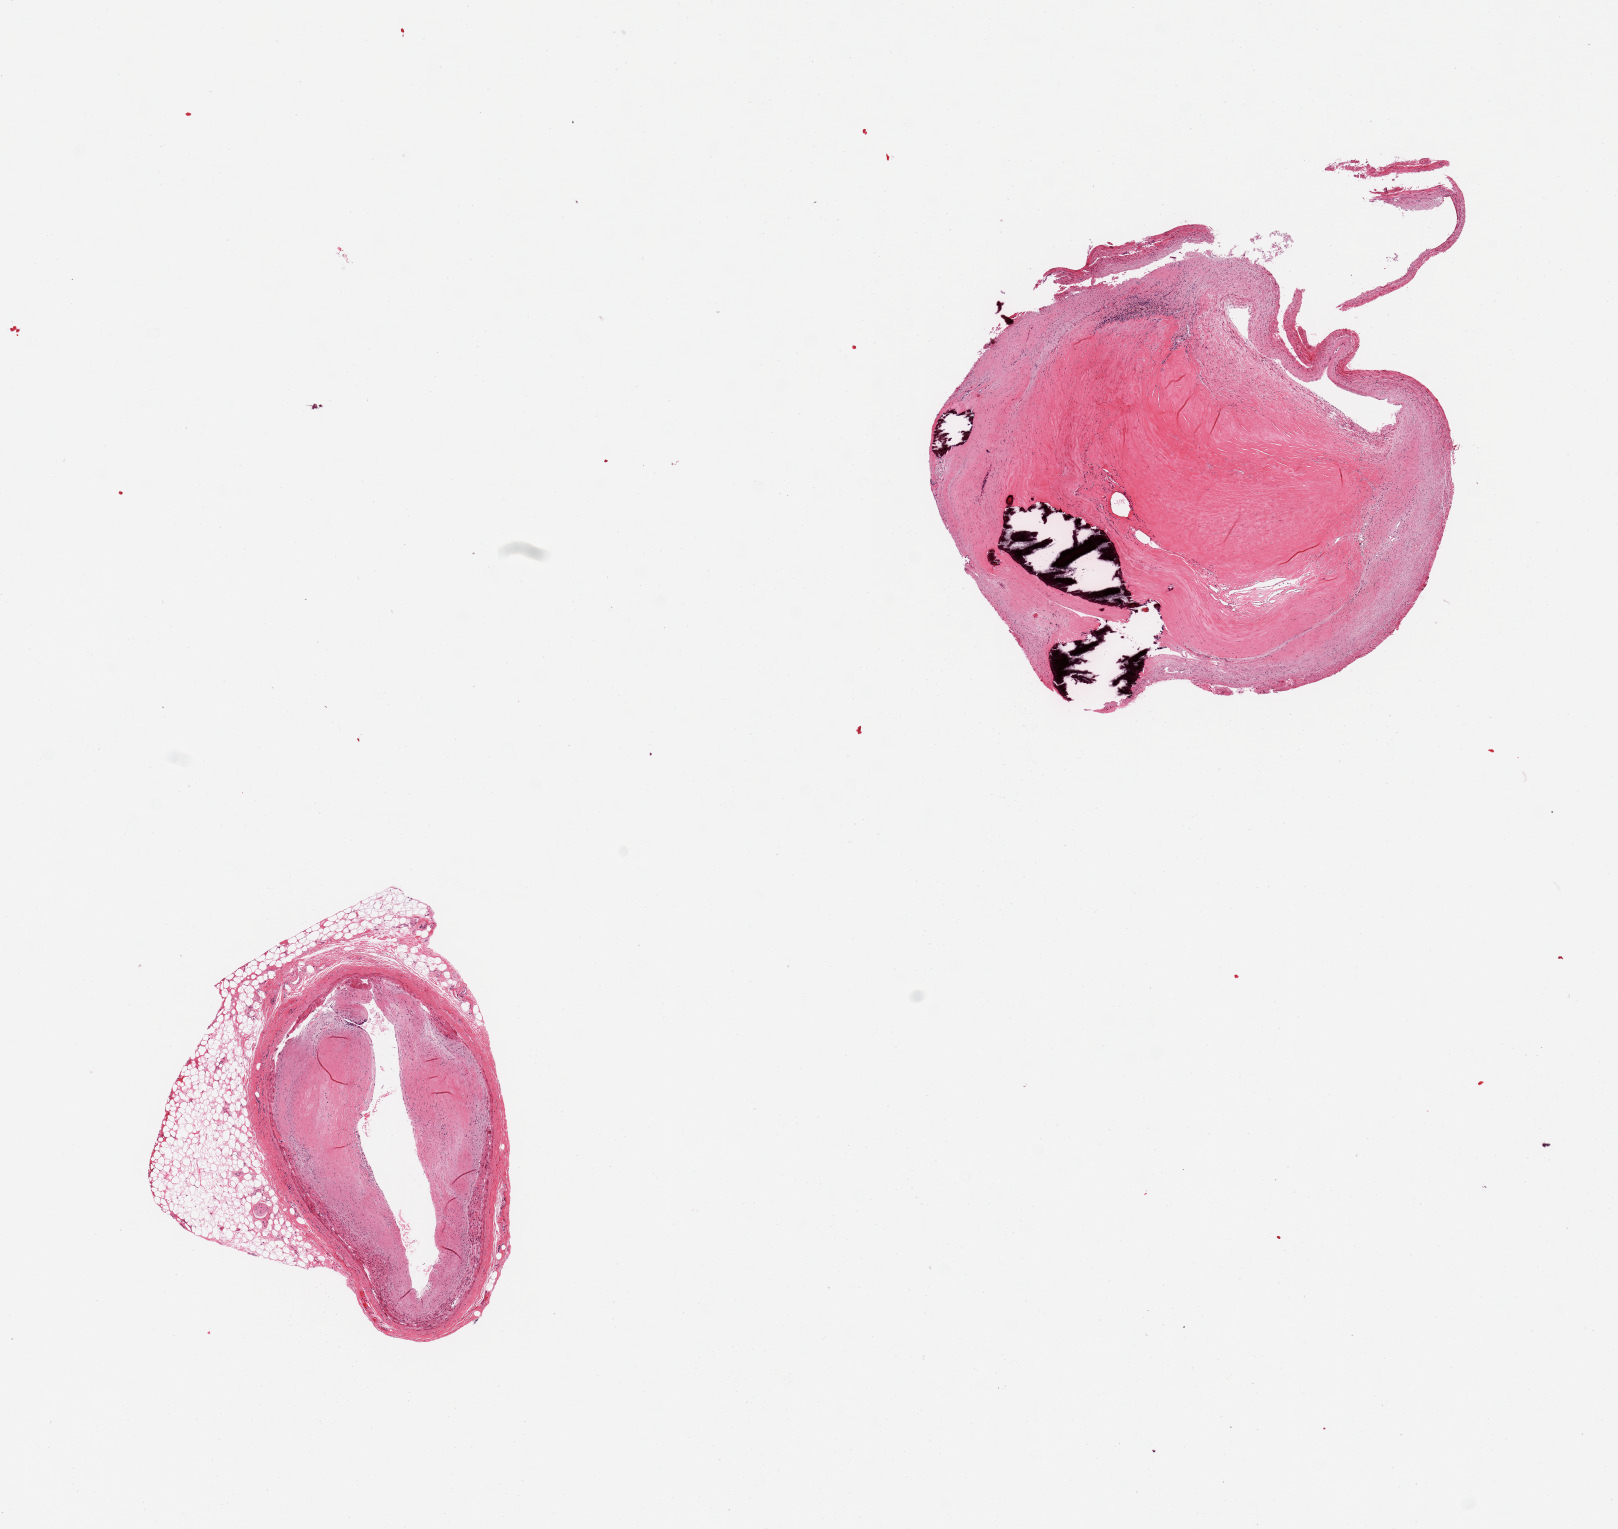
Hematoxylin and eosin (H&E) whole-slide image — a low-resolution overview of the entire scanned area, about 12.8 x 12.1 mm, PAXgene-fixed paraffin-embedded (PFPE) section, sampled site (target tissue): coronary artery, donor tissue sample. Donor: male.
Review note (as recorded): 2 pieces, significant calcific atherosclerosis (? orientation), smaller piece with atherosclerosis and narrowing of the lumen by >50% and partial rim of fat.